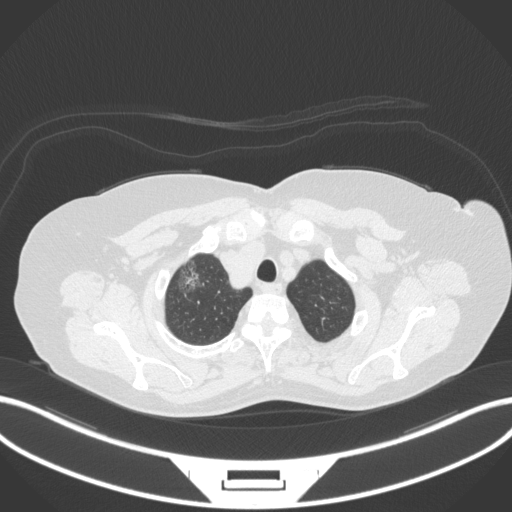
Chest CT, one axial slice. Position 310 of 365 along the scan axis. Reconstruction kernel B31f. 120 kVp. Lung window (W 1500 / L -600 HU). 512 × 512 image matrix, field of view 400 × 400 mm. Female patient, age 62 years. From the clinical record (not read from this slice): clinical TNM (as recorded): T1c N0 M0.
Annotated regions visible in this slice (rectangle marked by the reading radiologist):
- lung tumour (recorded histology: adenocarcinoma): bounding box [x1, y1, x2, y2] px = [173, 259, 208, 302]